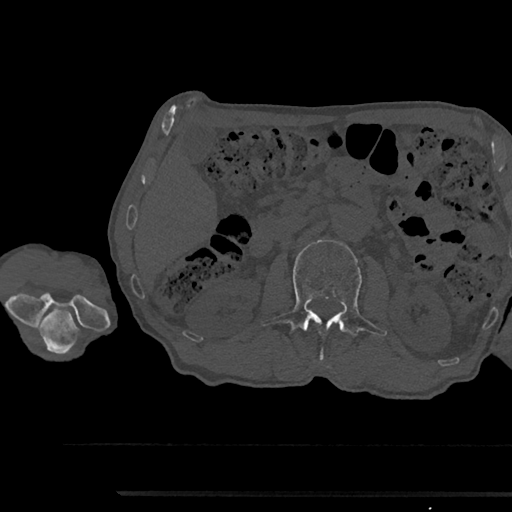
CT including the spine, one axial slice; reconstruction kernel Br40s/3; bone window (W 1800 / L 400 HU); 0.5 mm slice thickness; 512 × 512 image matrix, field of view 367 × 367 mm. Male patient, age 79 years. From the clinical record (not read from this slice): primary cancer: prostate.
Annotated regions visible in this slice (semi-automatically segmented with operator editing):
- L2 vertebra: box from (x=260, y=240) to (x=387, y=363) px